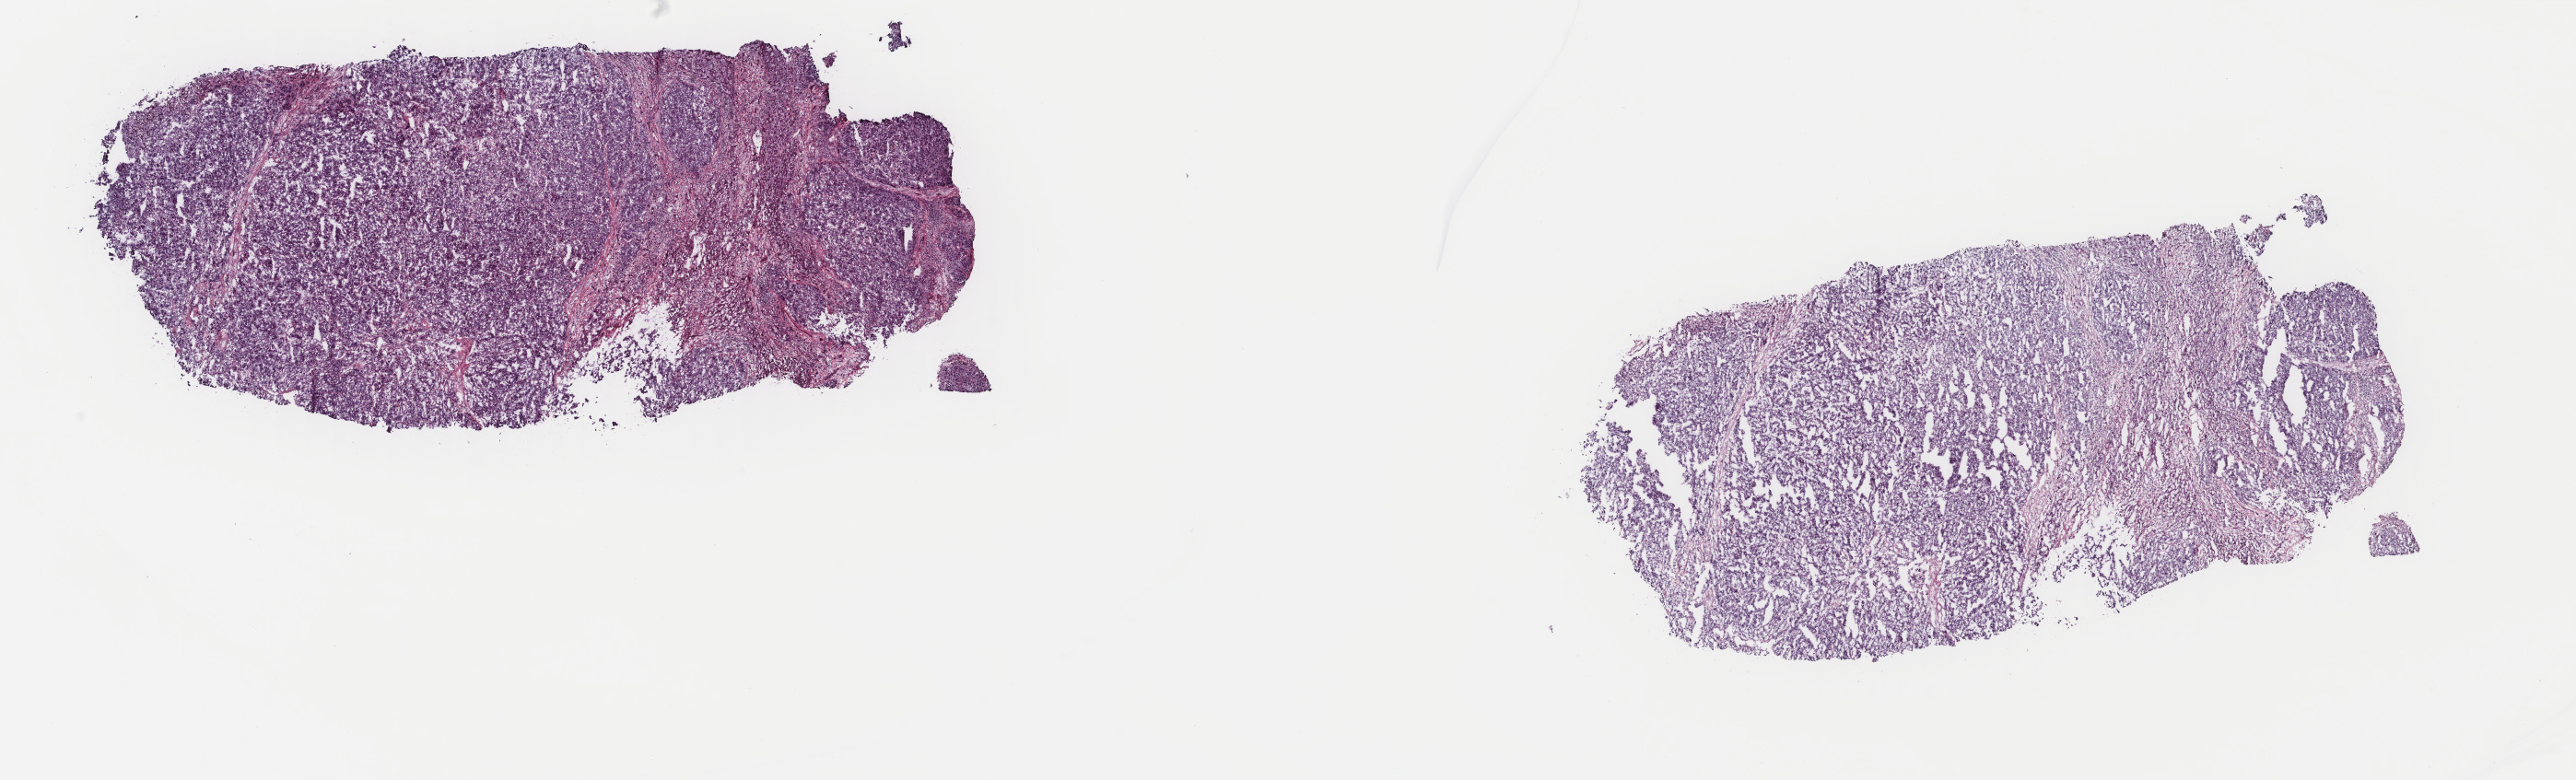
Whole-slide histology image, H&E, whole scanned area (about 22.2 x 6.7 mm, acquisition: 40x scan) shown as a low-resolution overview; frozen section from the top of the tissue portion; liver, primary tumour sample. Patient: male, age at initial diagnosis 63 years. Slide review estimates, as recorded: tumour cells 75%, tumour nuclei 80%.
Diagnosis: Hepatocellular carcinoma, NOS.